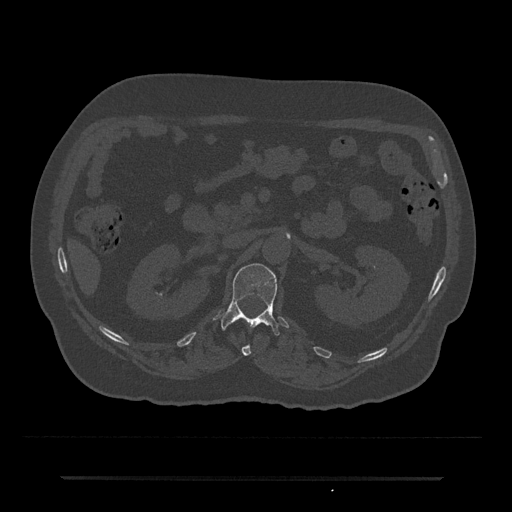
CT including the spine, one axial slice; slice 78 of 797 in the series (ordered by position); reconstruction kernel Br40s/3; 120 kVp; bone window (W 1800 / L 400 HU); 512 × 512 image matrix, field of view 437 × 437 mm. Male patient, age 69 years. From the clinical record (not read from this slice): primary cancer: prostate.
Outlined on this slice (semi-automatic segmentation, software-assisted and operator-edited):
- L1 vertebra: box from (x=221, y=263) to (x=280, y=336) px
- T12 vertebra: (x=241, y=345)–(x=251, y=356)